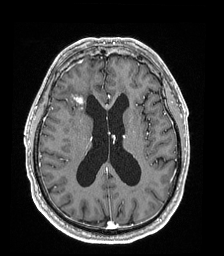
Brain MRI from a brain-tumour surgery series, one axial slice. Slice 84 of 192 in the series (ordered by position). T1-weighted post-contrast. 1 mm slice thickness. 224 × 256 image matrix, field of view 224 × 256 mm. Case-level facts recorded for this patient, not image findings: histopathology: Astrocytoma; WHO grade: 4.
Annotated regions visible in this slice (manually delineated by an expert):
- tumour: bounding box (x1, y1, x2, y2) in pixels: (75, 95, 84, 105)